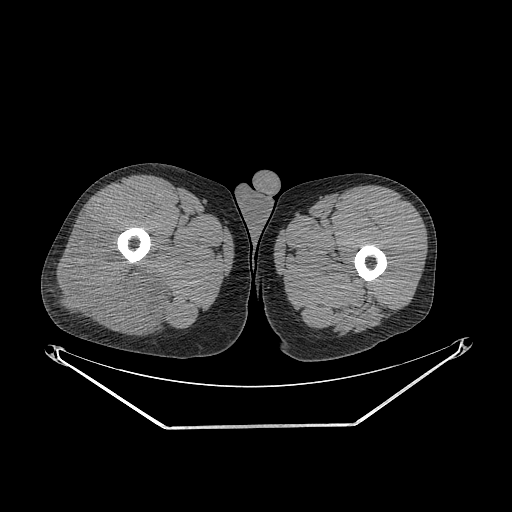
CT of an extremity soft-tissue mass (from a PET/CT study), one axial slice; position 259 of 267 along the scan axis; 140 kVp; soft-tissue window (W 400 / L 40 HU); 3.75 mm slice thickness; 512 × 512 image matrix. Male patient. From the clinical record (not read from this slice): histological type: poorly differentiated synovial sarcoma; grade: high; site of the primary tumour: right buttock.
Annotated regions visible in this slice (expert contour drawn on MRI and transferred to this co-registered scan by the dataset authors):
- gross tumour volume including surrounding oedema: bounding box [x1, y1, x2, y2] px = [53, 219, 163, 334]
- gross tumour volume (mass): [53, 219, 161, 334]